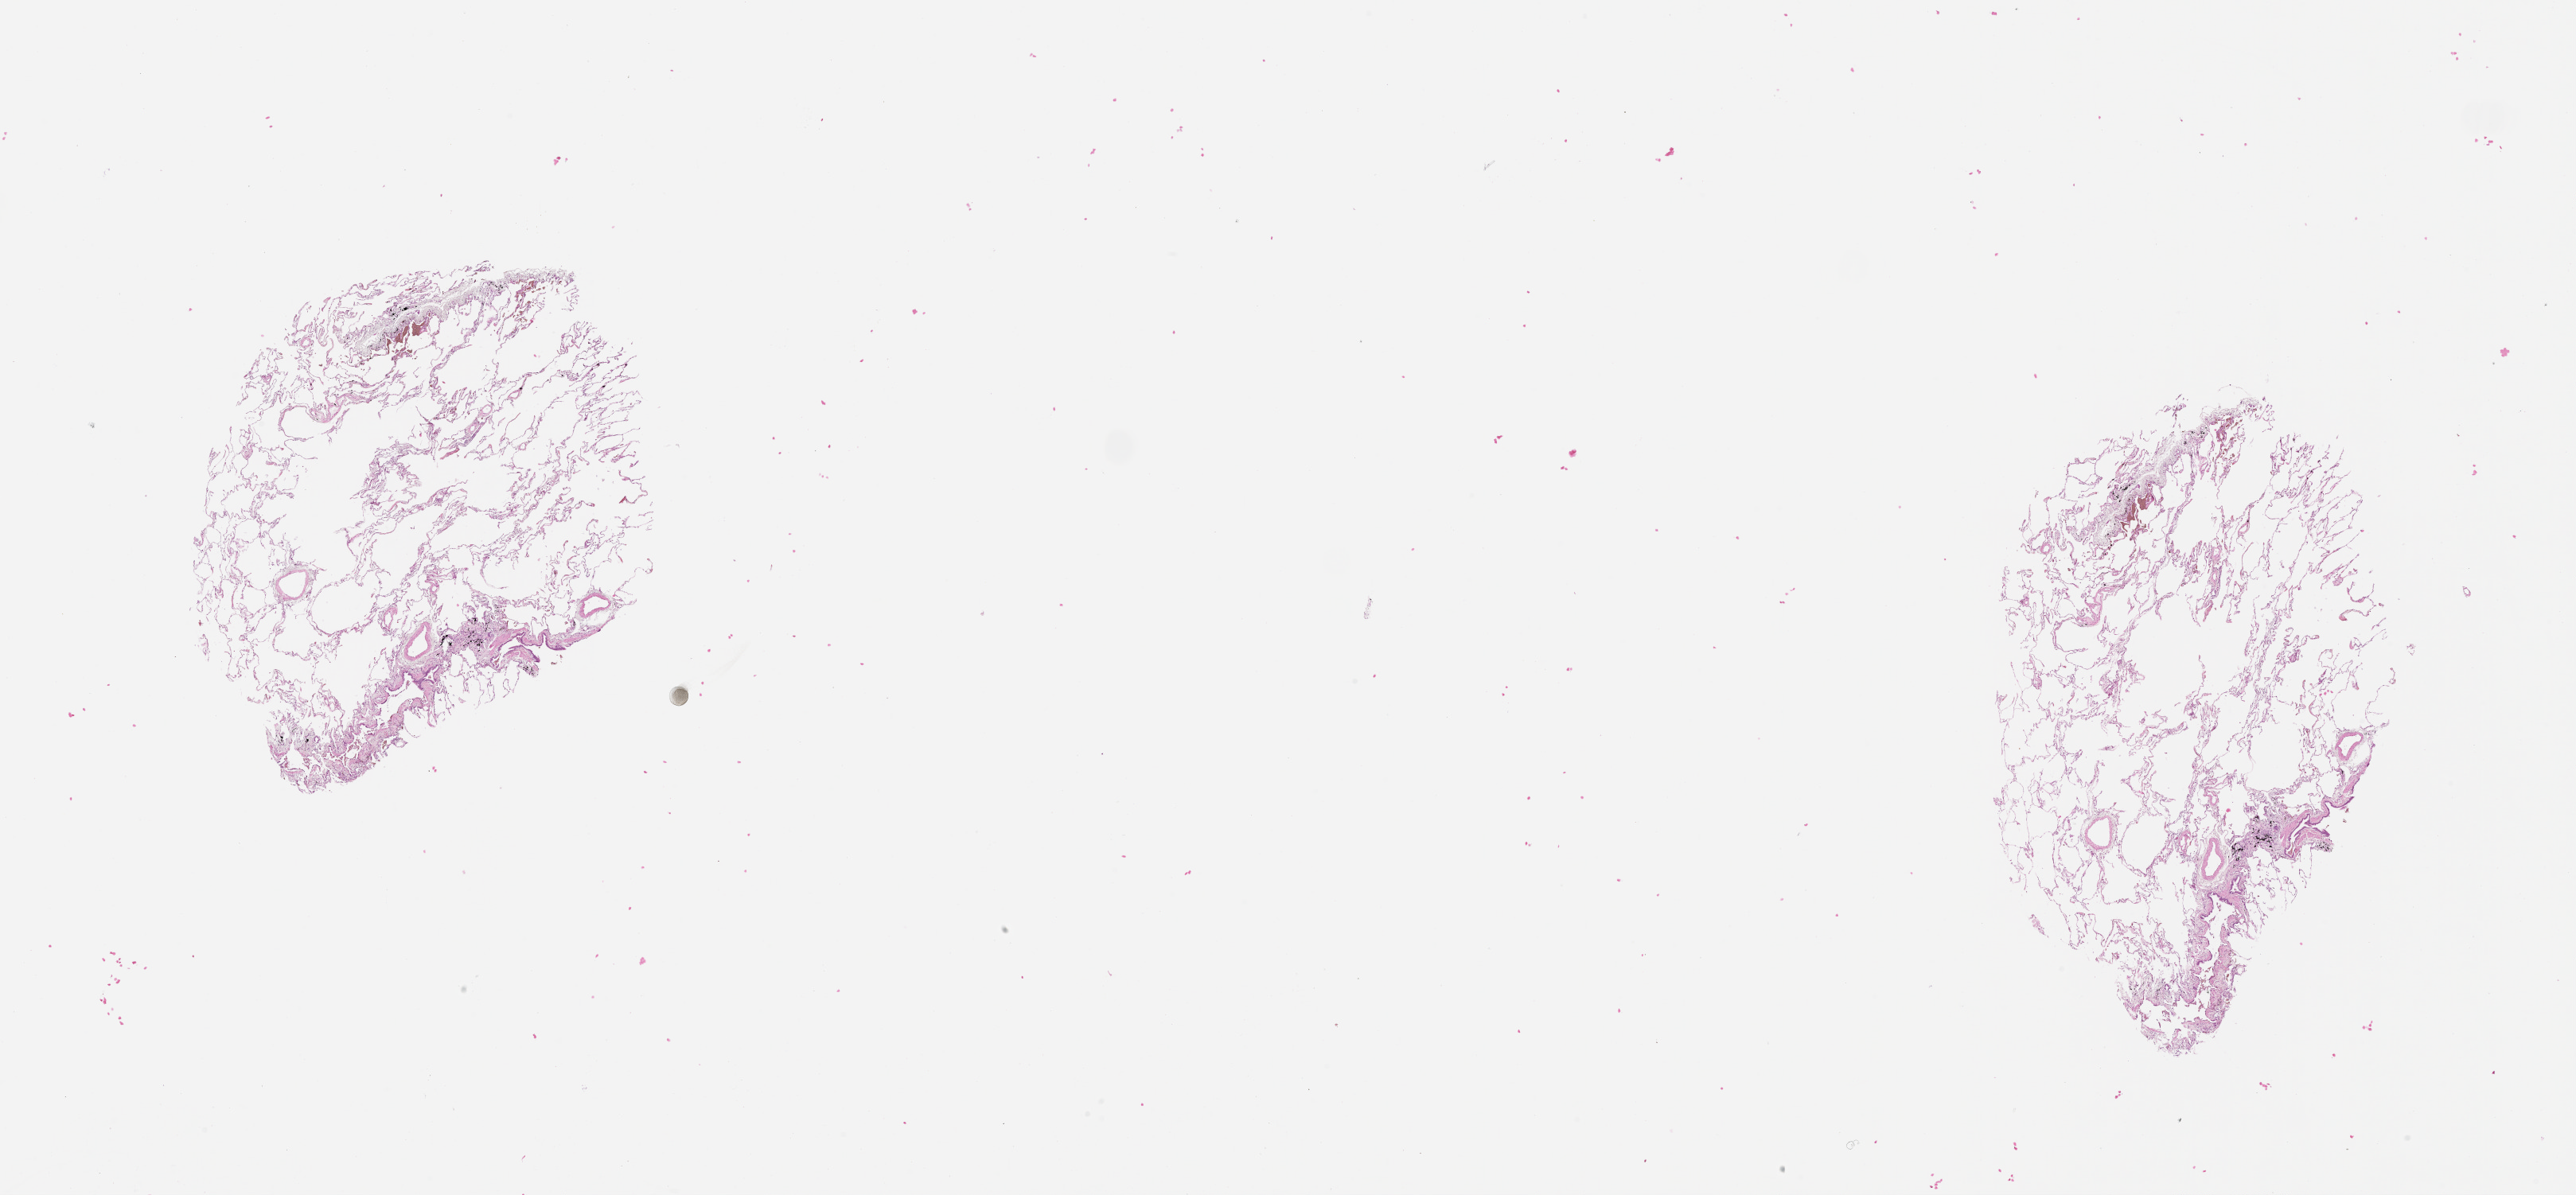
Digitized H&E-stained tissue section (whole slide) — shown as a low-resolution overview of the whole scanned area (about 26.1 x 12.1 mm, from a 20x scan). Normal (non-tumour) tissue sample, sampled site: lung. Patient: female, age 63 years.
• this section: normal (non-tumour) tissue from the same patient
• patient diagnosis: Adenocarcinoma, NOS